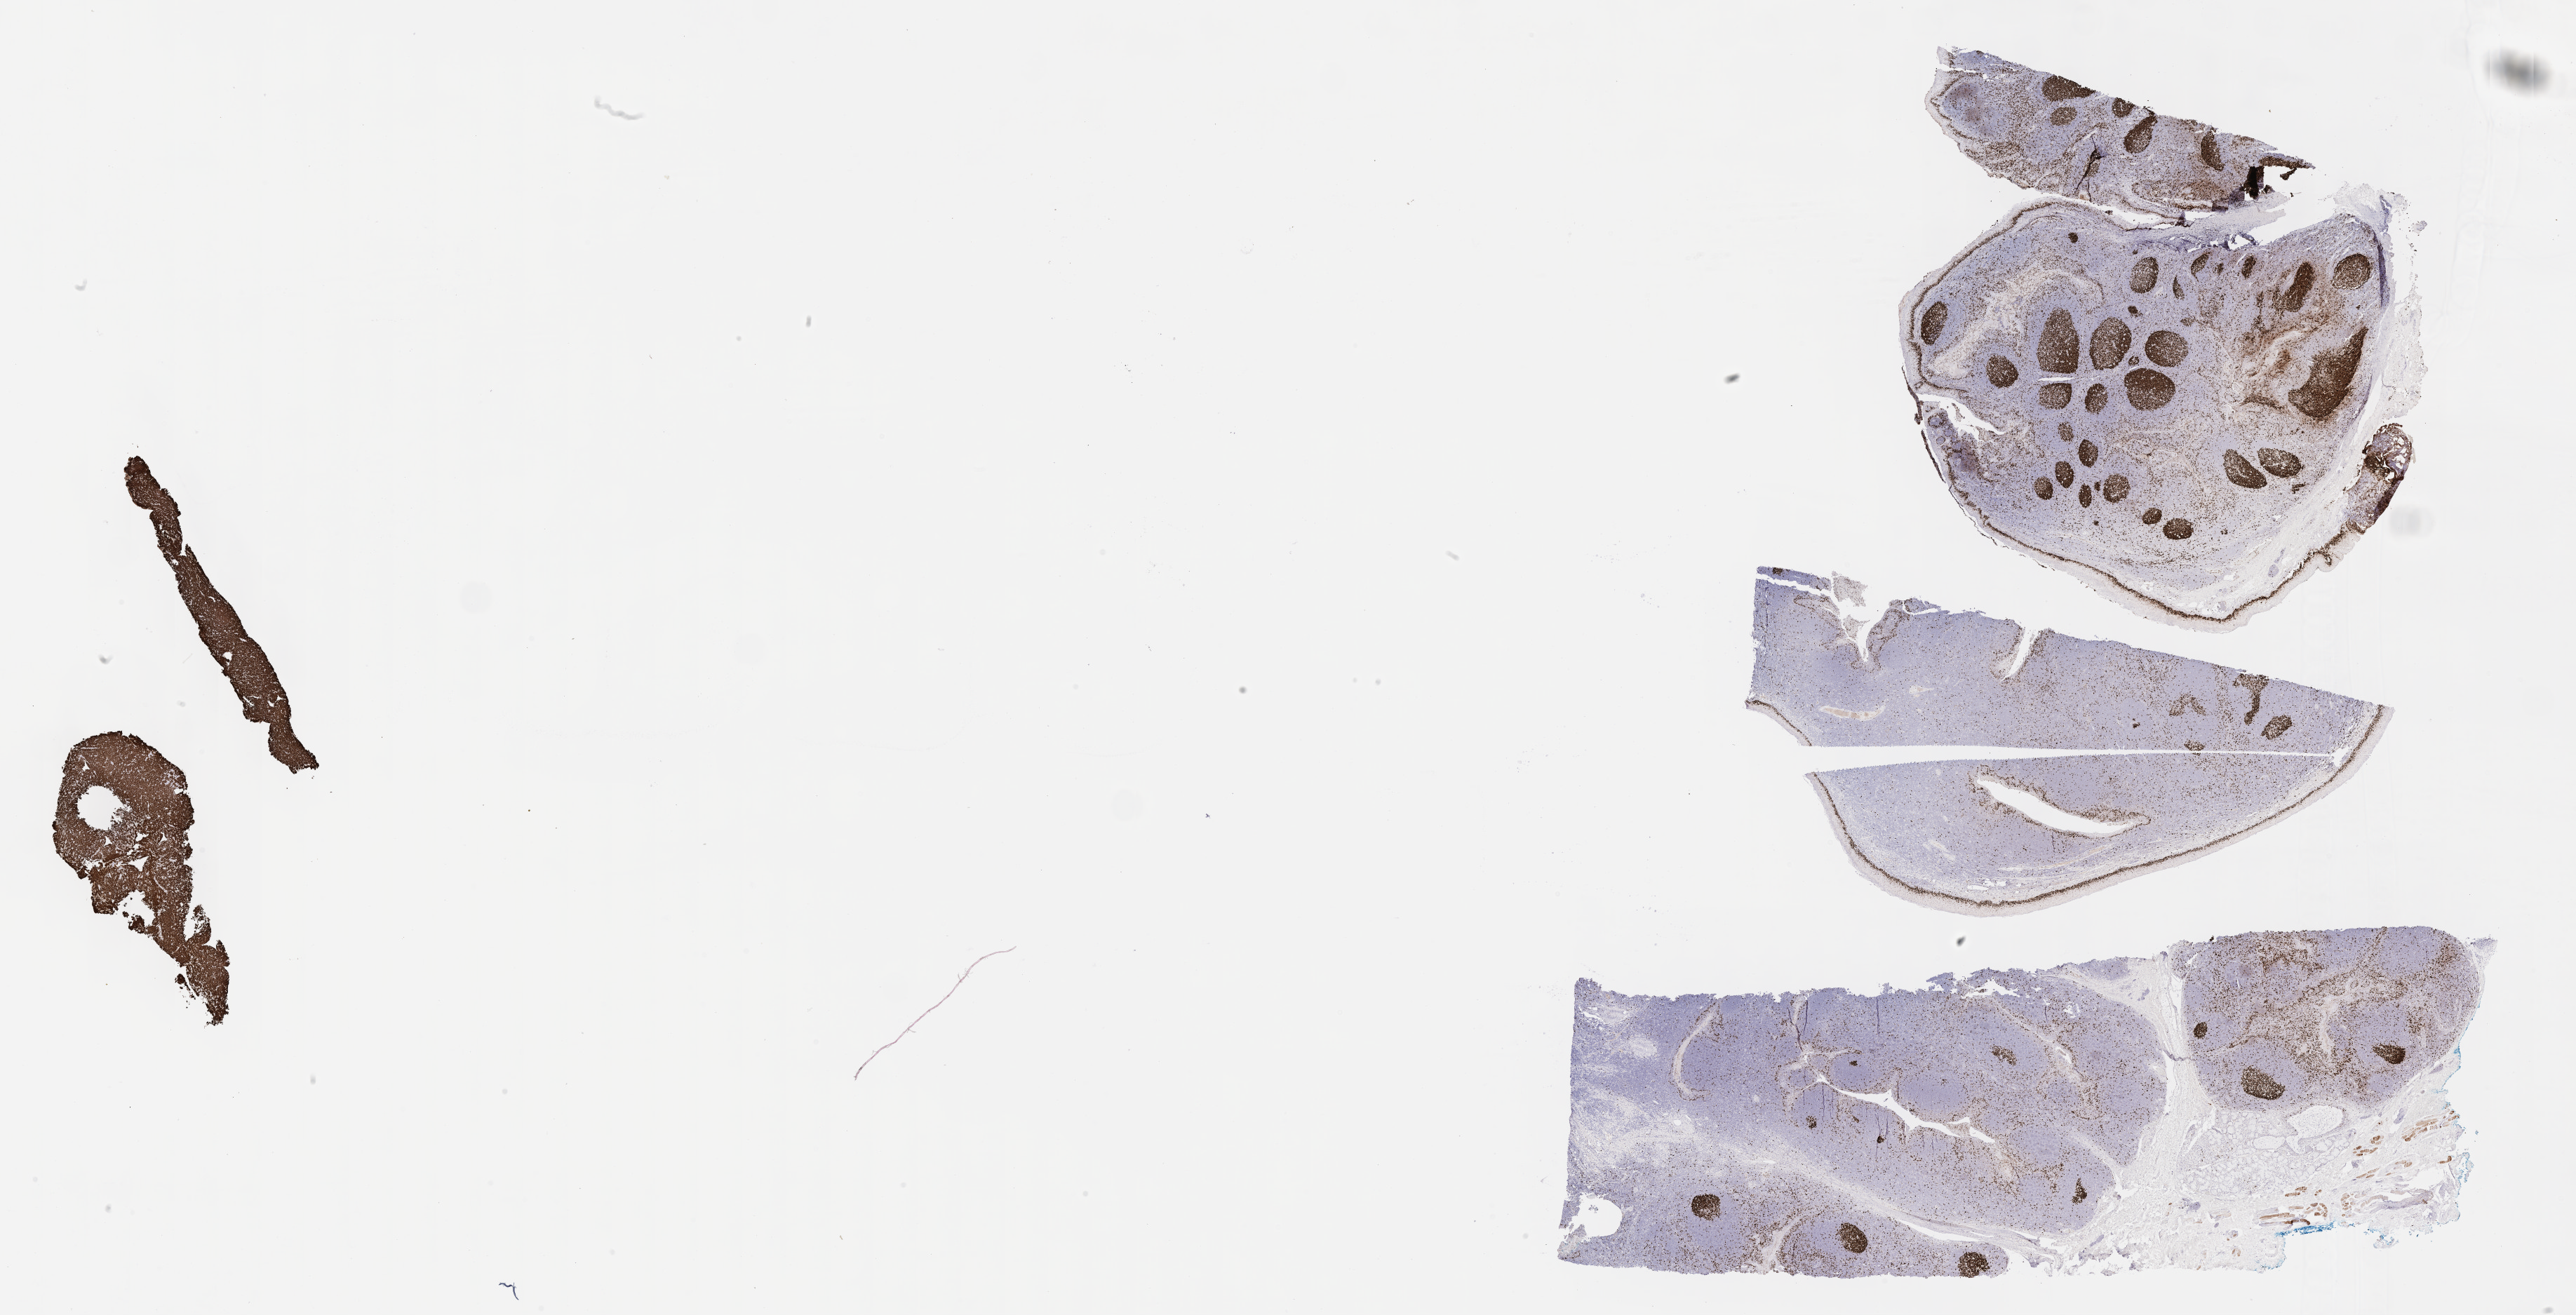
Whole-slide image, immunohistochemical stain for Ki-67 — a low-resolution overview of the entire scanned area, about 29.7 x 15.2 mm; tumor tissue. Patient: male, age at initial diagnosis 8 years.
Diagnosis: Burkitt lymphoma, NOS.